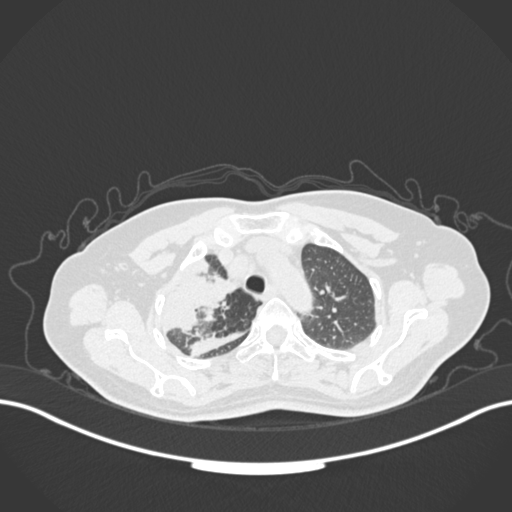
Chest CT, one axial slice. Slice 128 of 177 in the series (ordered by position). Reconstruction kernel B30f. 120 kVp. Lung window (W 1500 / L -600 HU). 1 mm slice thickness. 512 × 512 image matrix. Female patient, age 60 years. Case-level facts recorded for this patient, not image findings: clinical TNM (as recorded): T3 N1 M1.
Annotated regions visible in this slice (bounding box drawn by a radiologist):
- lung tumour (recorded histology: adenocarcinoma): box from (x=153, y=257) to (x=243, y=341) px